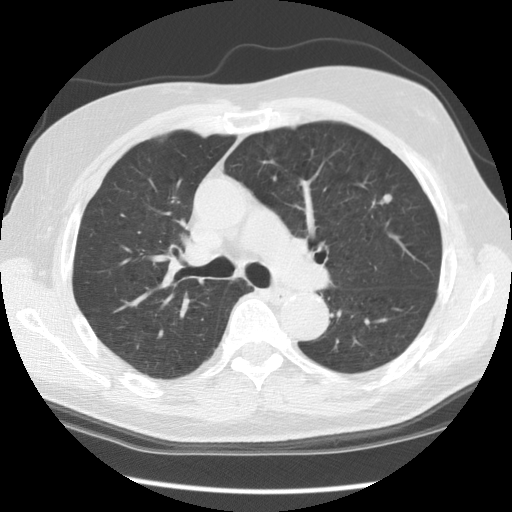
Axial slice from a low-dose chest CT screening exam, second screening round (one year after baseline), lung window (W 1500 / L -600 HU), slice 88 of 140 in the series. Male, age 70 years at enrolment. Current smoker at enrolment.
• Expert-annotated lung lesion, bounding box (x1, y1, x2, y2) in pixels: (342, 181, 403, 236).
• The screening reader recorded 3 non-calcified nodules or masses ≥4 mm on this exam (right lower lobe, left upper lobe, left upper lobe); which of them this box marks is not recorded.
• Official screen result: positive, other.
• Participant outcome: lung cancer diagnosed 396 days after this screen — adenocarcinoma, NOS, left upper lobe, moderately differentiated (G2), stage IIIA (AJCC 6th edition), 17 mm at pathology.